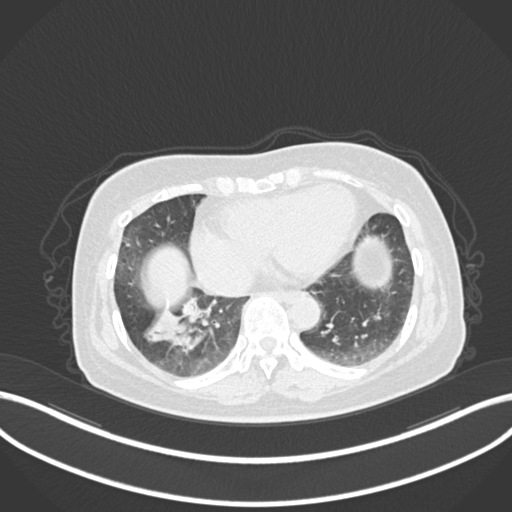
Chest CT, one axial slice; slice 37 of 222 in the series (ordered by position); 120 kVp; lung window (W 1500 / L -600 HU); 512 × 512 image matrix. Patient: female, 67 years. Case-level facts recorded for this patient, not image findings: clinical TNM (as recorded): T1c N1 M0.
Outlined on this slice (rectangle marked by the reading radiologist):
- lung tumour (recorded histology: adenocarcinoma): box from (x=137, y=296) to (x=218, y=349) px